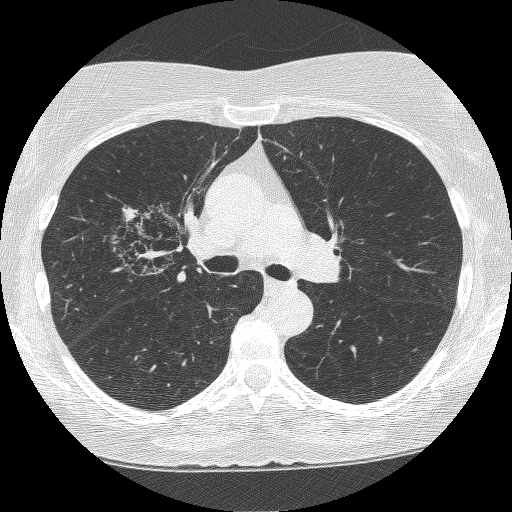
Low-dose screening chest CT, axial slice; second annual screen; lung window (W 1500 / L -600 HU); 1.25 mm slice thickness; lung (sharp) reconstruction kernel (BONE); slice 153 of 249 in the series. Female participant, aged 64 years at enrolment.
- Expert reader's lesion annotation, bounding box [x1, y1, x2, y2] px = [115, 205, 205, 290].
- The screening reader recorded 4 non-calcified nodules or masses ≥4 mm on this exam (right upper lobe, right upper lobe, right upper lobe, left upper lobe); which of them this box marks is not recorded.
- Official screen result: positive, other.
- Participant outcome: lung cancer diagnosed 381 days after this screen (after the third annual screen) — adenocarcinoma, NOS, right upper lobe, right middle lobe, right hilum, stage IV (AJCC 6th edition), 85 mm at pathology.